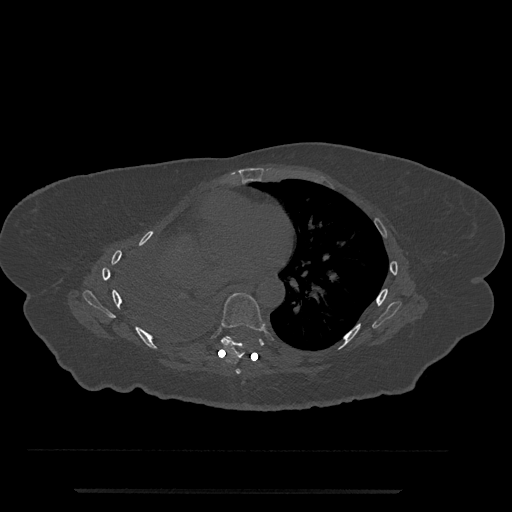
CT including the spine, one axial slice; position 434 of 797 along the scan axis; 120 kVp; bone window (W 1800 / L 400 HU); 512 × 512 image matrix, field of view 440 × 440 mm. Patient: female, 51 years. Case-level facts recorded for this patient, not image findings: primary cancer: neuro; vertebrae with lytic lesions (as recorded): T8.
Outlined on this slice (semi-automatically segmented with operator editing):
- T6 vertebra: bounding box <235,369,241,374> (left, top, right, bottom; pixels)
- T7 vertebra: <221,293,266,358>
- T8 vertebra: <223,336,230,339>